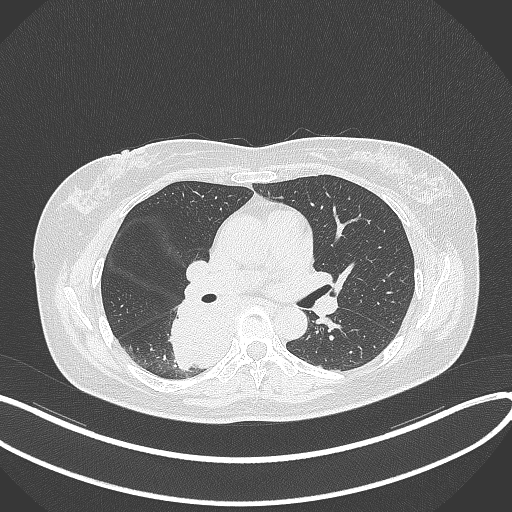
Chest CT, one axial slice. Slice 203 of 331 in the series (ordered by position). Reconstruction kernel B70f. Lung window (W 1500 / L -600 HU). 1 mm slice thickness. 512 × 512 image matrix, field of view 400 × 400 mm. Patient: female, 54 years. Case-level facts recorded for this patient, not image findings: clinical TNM (as recorded): T4 N0 M0.
Outlined on this slice (bounding box drawn by a radiologist):
- lung tumour (recorded histology: adenocarcinoma): bounding box (x1, y1, x2, y2) in pixels: (164, 296, 234, 371)